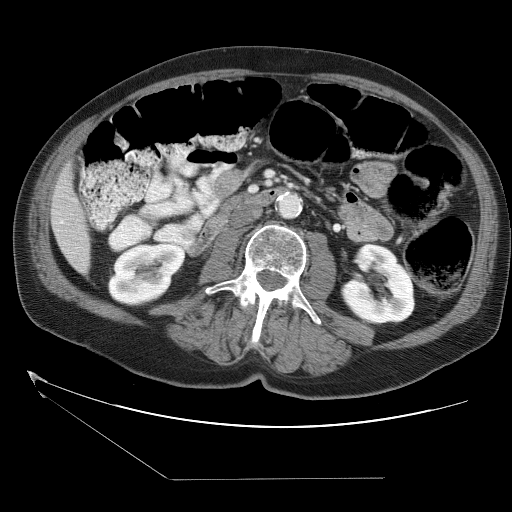
Contrast-enhanced abdominal CT (liver protocol), one axial slice; slice 4 of 38 in the series (ordered by position); reconstruction kernel STANDARD; soft-tissue window (W 400 / L 40 HU); 5 mm slice thickness; 512 × 512 image matrix, field of view 400 × 400 mm. From the clinical record (not read from this slice): diagnosis: hepatocellular carcinoma (patient treated with transarterial chemoembolisation; whether this scan precedes or follows treatment is not stated here); TNM stage (as recorded): Stage-II; Child-Pugh class: A; tumour differentiation: moderately differentiated; tumour nodularity: multinodular.
Structures marked on this image (semi-automatic segmentation, software-assisted and operator-edited):
- liver parenchyma outside the tumour (the mass and vessels are separate outlines, so this box may not span the whole liver): bounding box (x1, y1, x2, y2) in pixels: (50, 163, 90, 272)
- liver vessels: (59, 220, 64, 224)